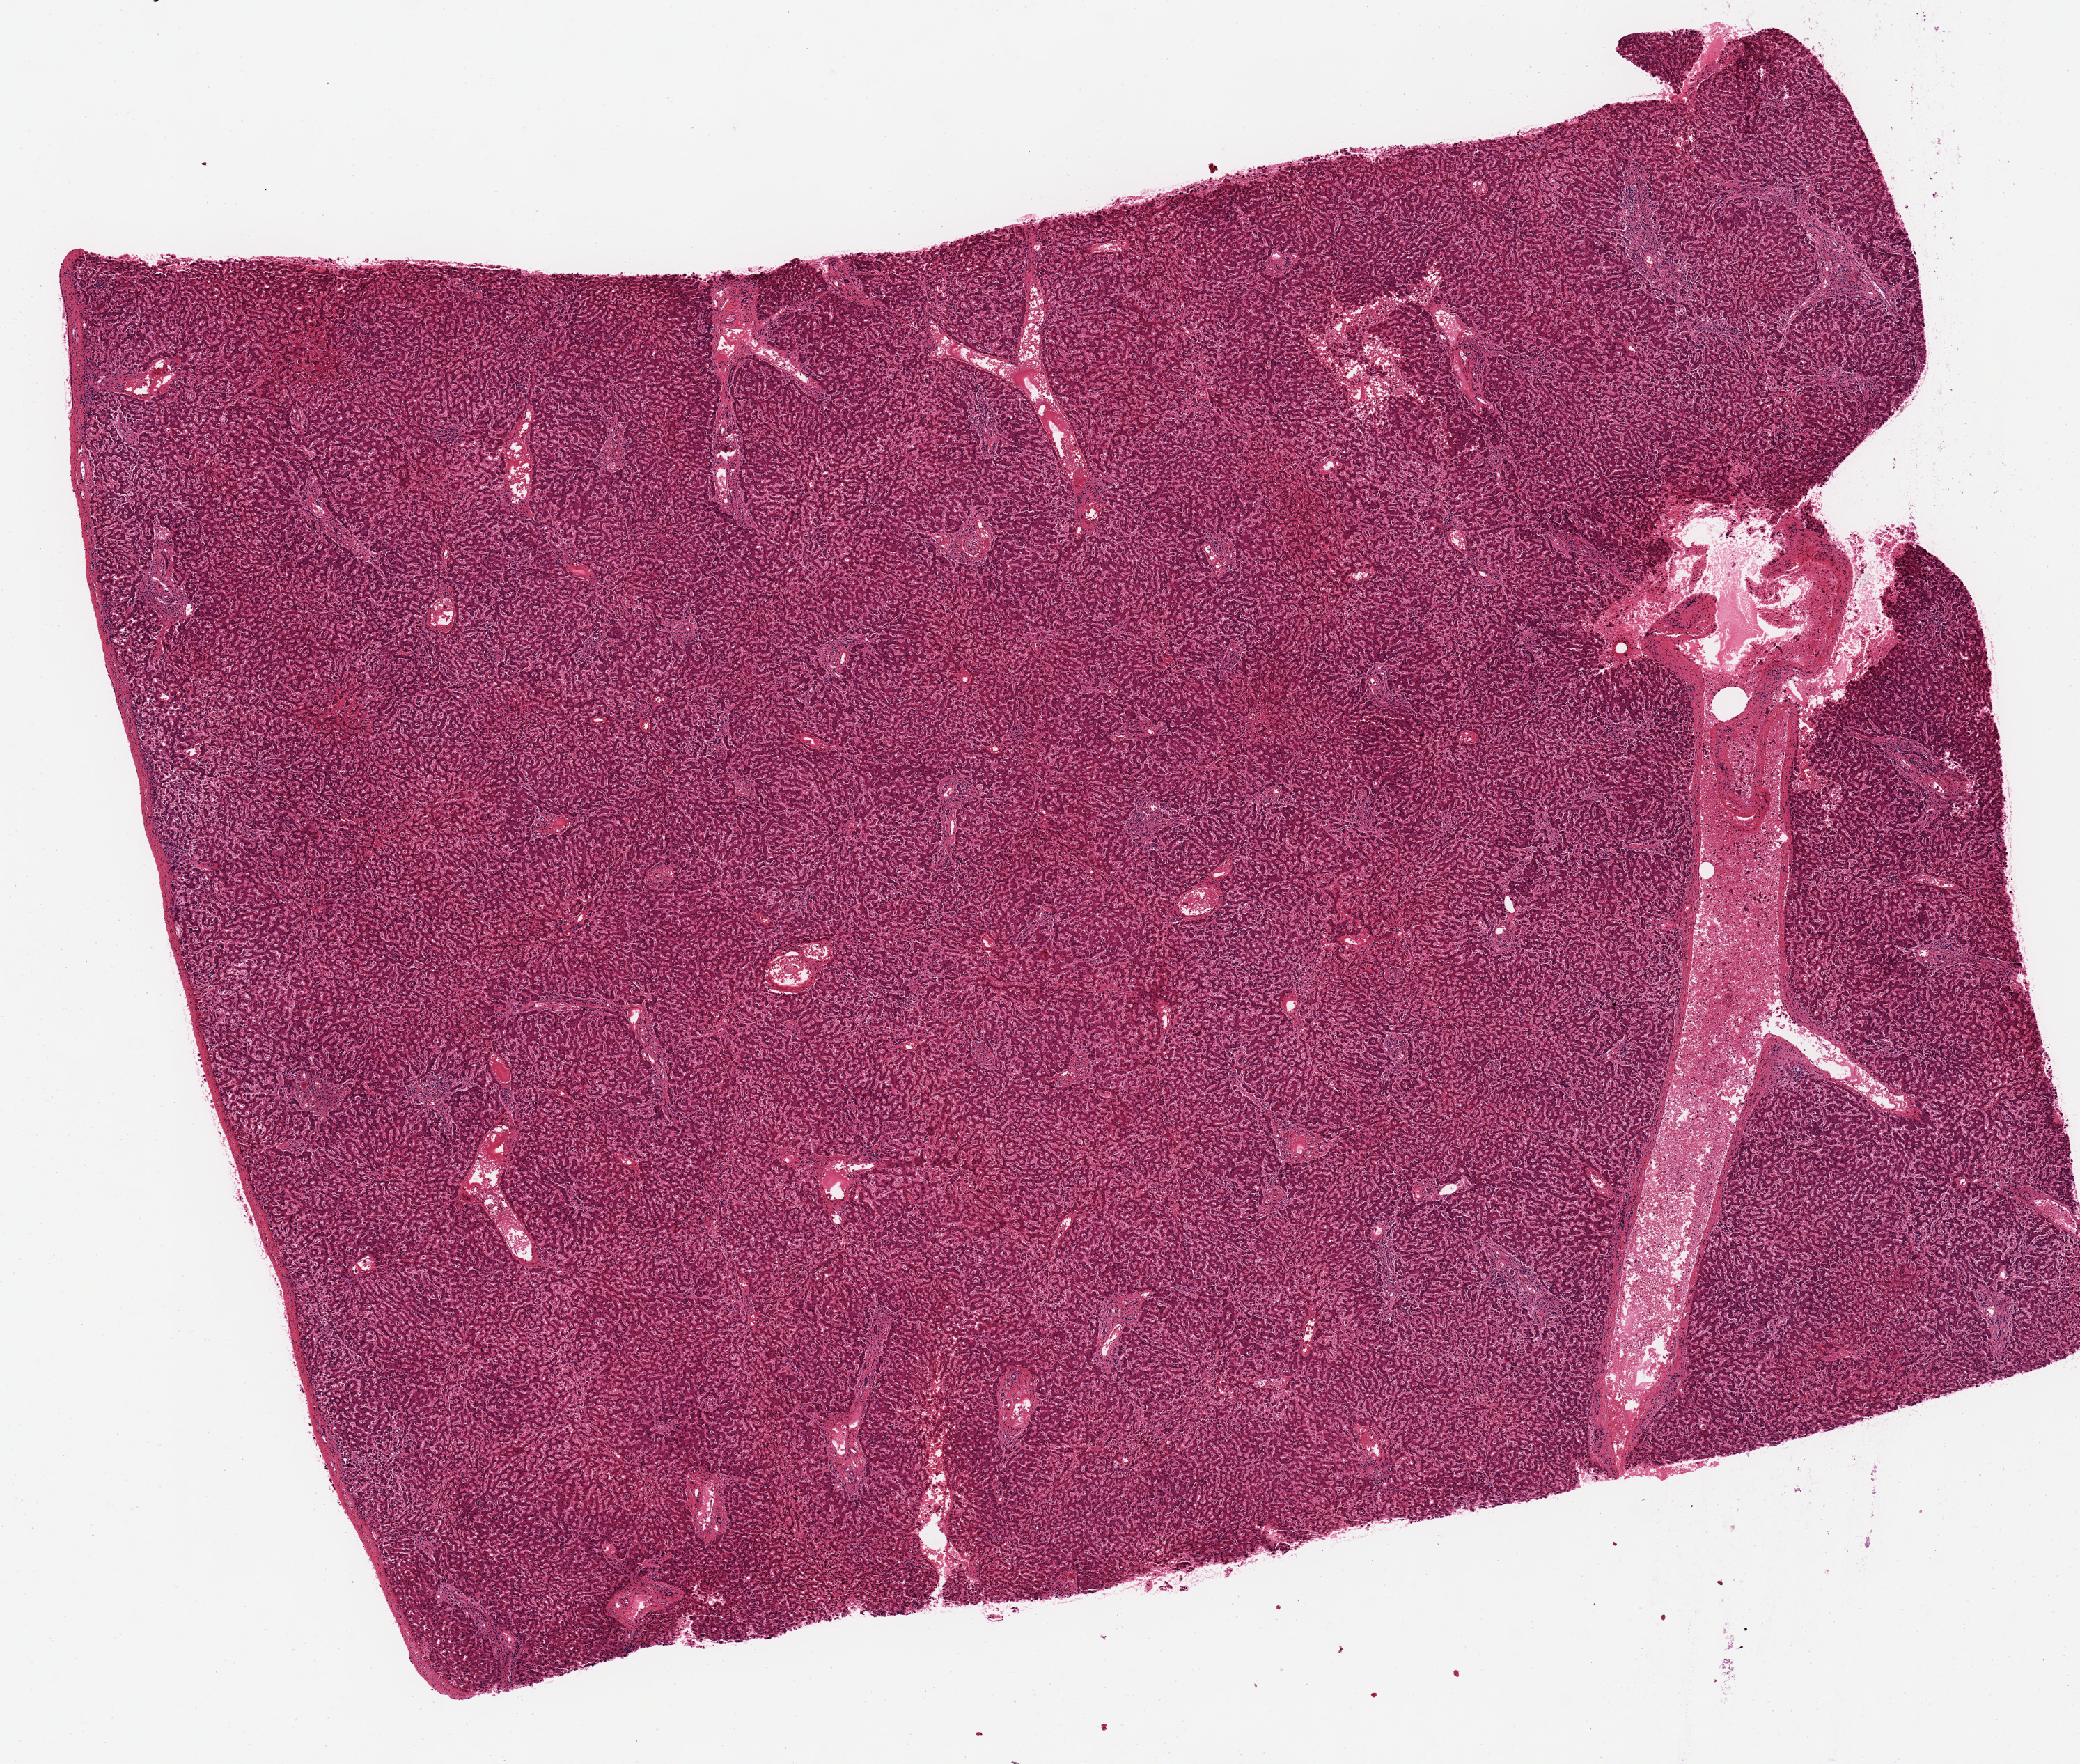
H&E whole-slide image, a low-resolution overview of the entire scanned area, about 11.8 x 10.0 mm (slide scanned at 20x). PAXgene-fixed, paraffin-embedded tissue. Section of liver (target tissue). Tissue donor sample. Female donor.
Review note (as recorded): Subcapsular aliquot (9 .5 x 7.5mm aqliquot).